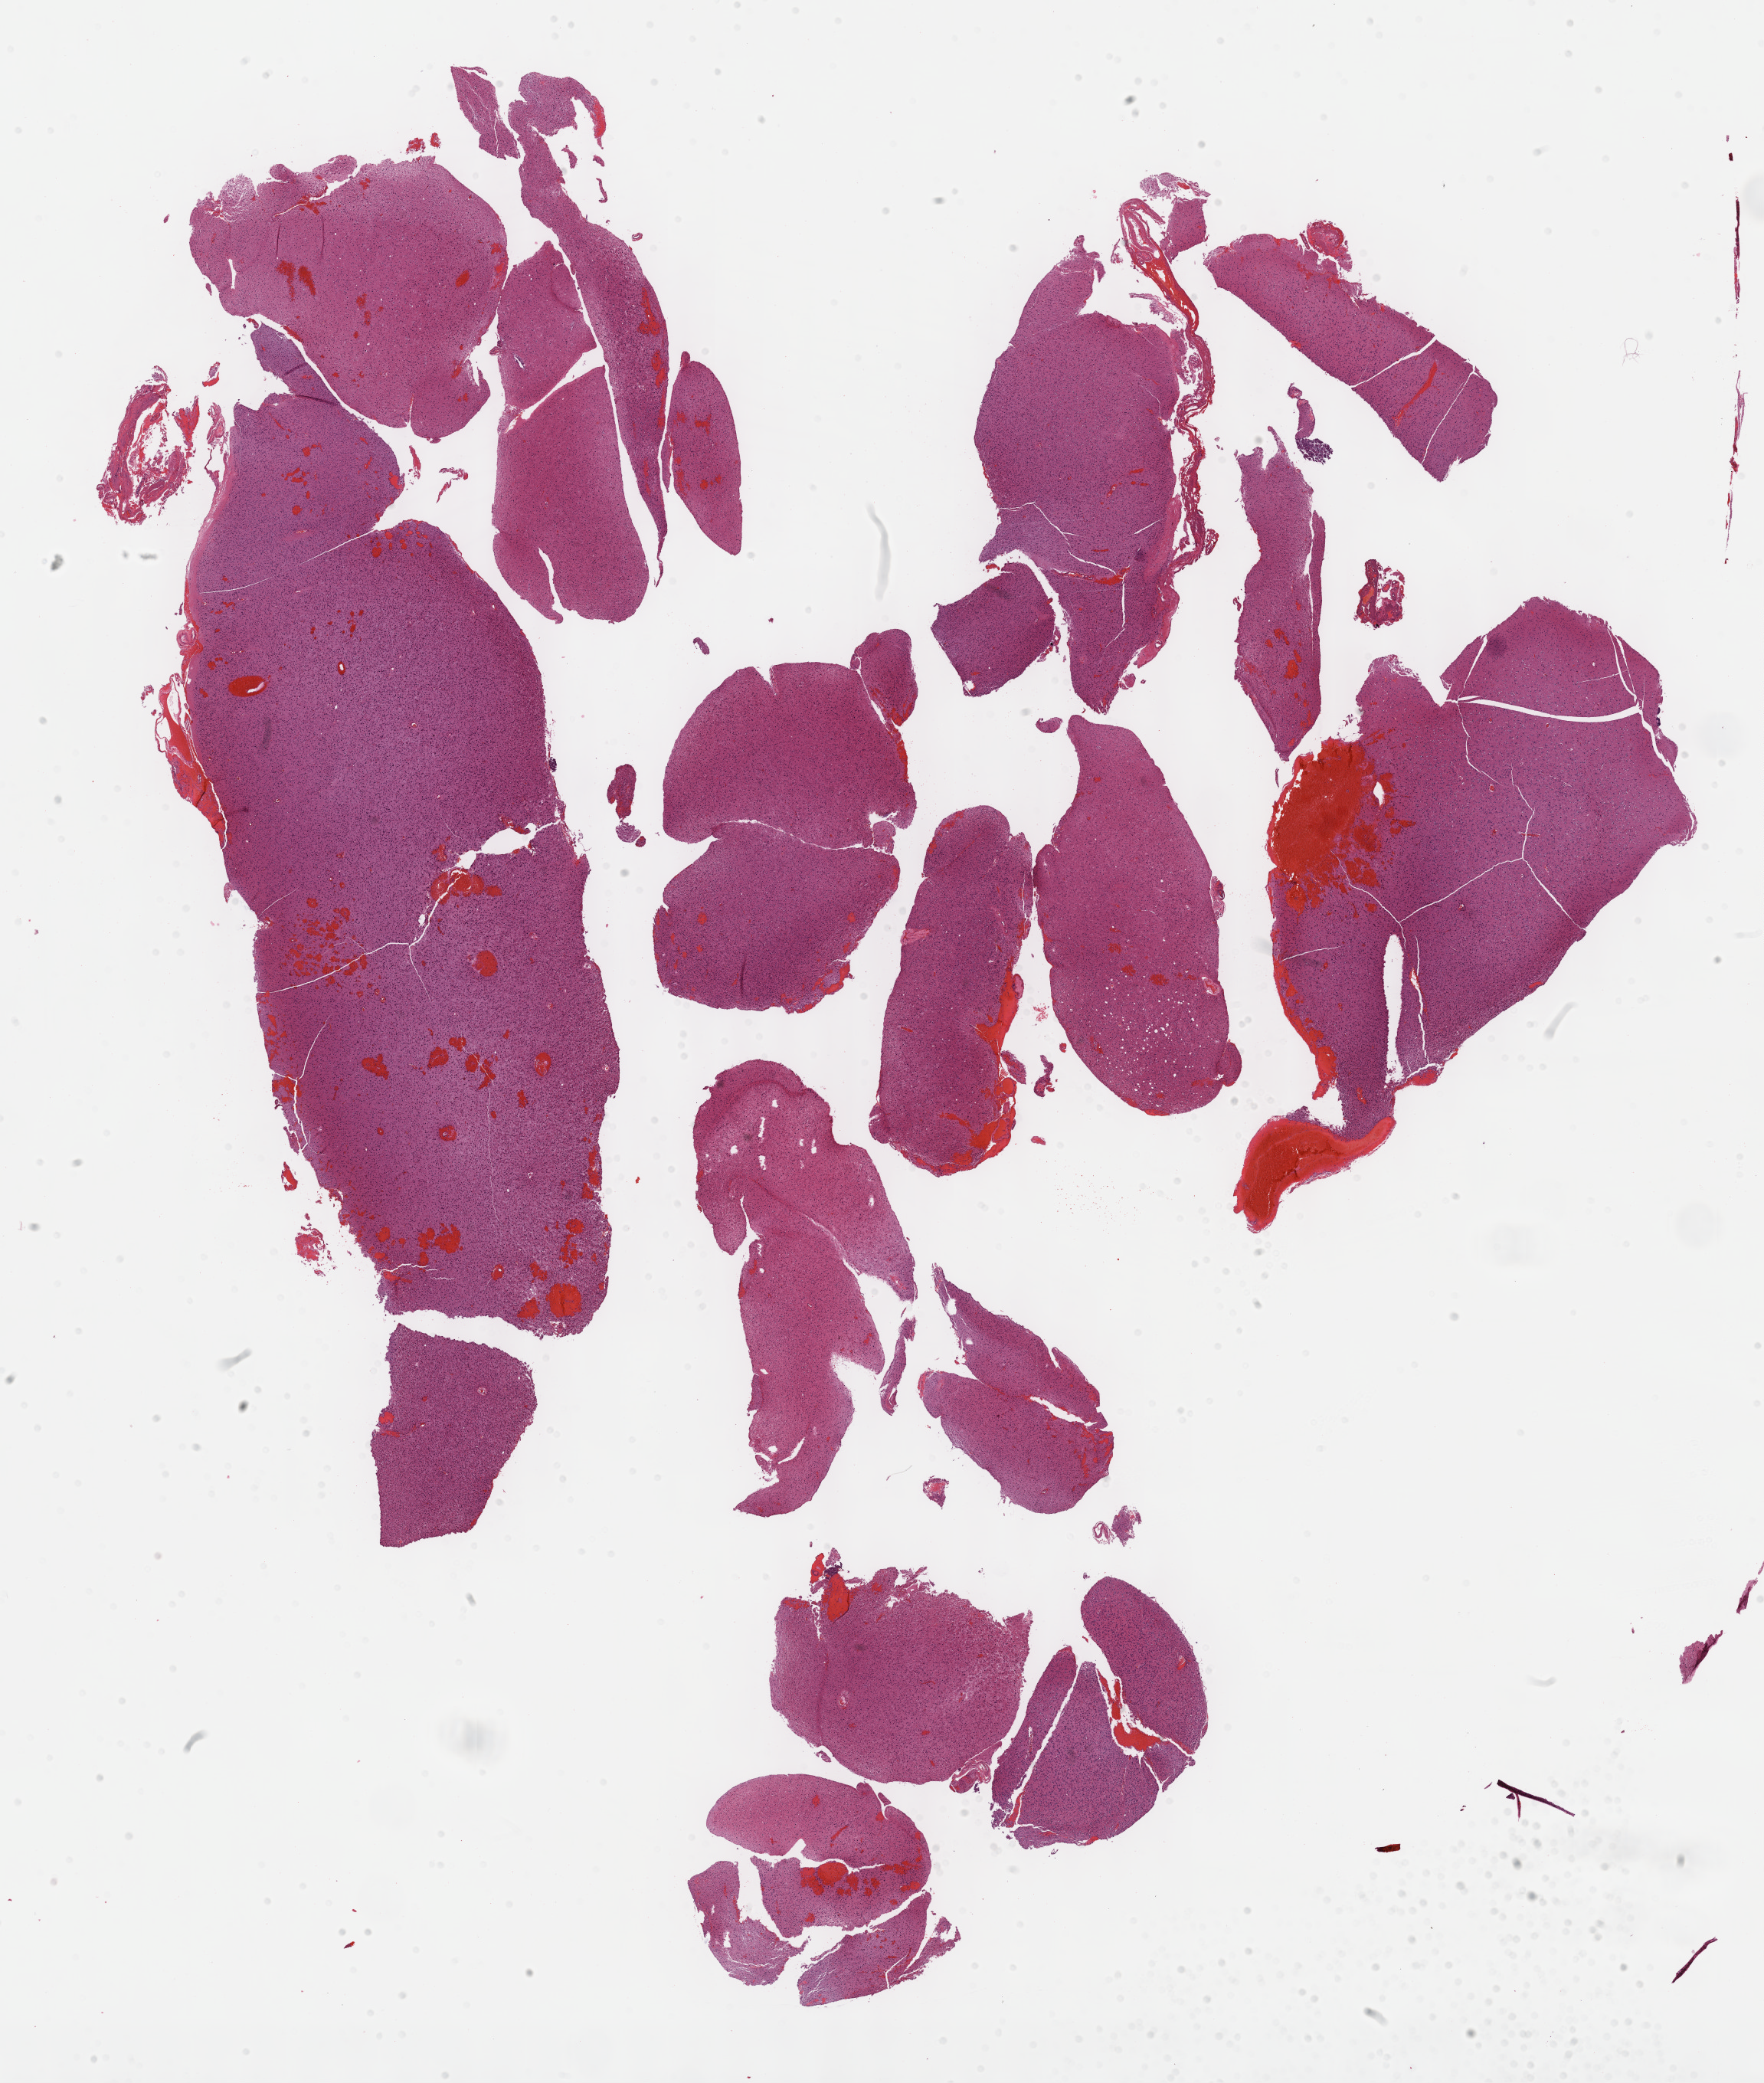
Digitized H&E tissue section (whole slide), a low-resolution overview of the entire scanned area, about 18.6 x 22.0 mm; formalin-fixed paraffin-embedded (FFPE) diagnostic section; brain, primary tumour sample. Male patient; age at initial diagnosis 42 years. Histologic grade: G2 (moderately differentiated).
Histologic diagnosis: Astrocytoma, NOS.